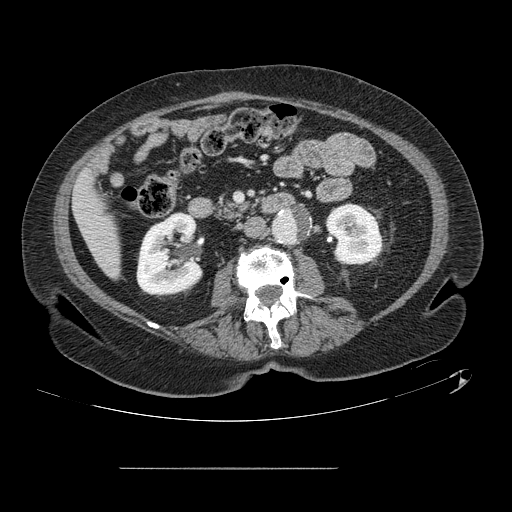
Contrast-enhanced abdominal CT, one axial slice; slice 29 of 148 in the series (ordered by position); intravenous contrast given; soft-tissue window (W 400 / L 40 HU); 2.5 mm slice thickness; 512 × 512 image matrix. Female patient, age 75 years. Case-level facts recorded for this patient, not image findings: diagnosis: colorectal cancer liver metastases, imaged before liver resection; multiple liver metastases: no.
Structures marked on this image (outlined manually by an expert reader):
- liver: box from (x=75, y=173) to (x=120, y=276) px
- planned liver remnant (the part of the liver to remain after resection): (x=75, y=173)–(x=120, y=276)